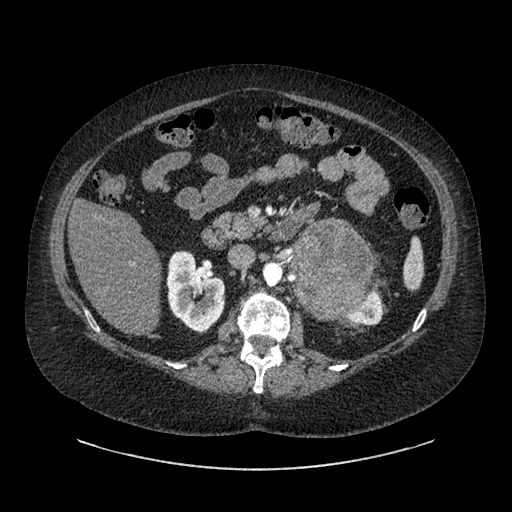
Contrast-enhanced abdominal CT, one axial slice. Position 527 of 769 along the scan axis. 120 kVp. Intravenous contrast given. Soft-tissue window (W 400 / L 40 HU). 512 × 512 image matrix, field of view 460 × 460 mm. Female patient, age 61 years. Case-level facts recorded for this patient, not image findings: diagnosis: adrenocortical carcinoma; tumour side: left adrenal; tumour size at pathology: 13 cm; Ki-67 index: 79 %; stage (as recorded): 2.
Annotated regions visible in this slice (semi-automatically segmented with operator editing):
- mass: bounding box (x1, y1, x2, y2) in pixels: (292, 222, 372, 317)